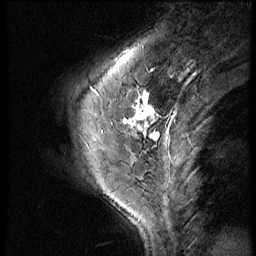
Breast MRI (dynamic contrast-enhanced), one sagittal slice; 3 images stored at this slice position (order not interpretable as contrast timing); 1.5 T; TE 4.2 ms, TR 9 ms; 2.5 mm slice thickness; 256 × 256 image matrix. Female patient, age 46 years. Case-level facts recorded for this patient, not image findings: setting: breast cancer imaged before/during neoadjuvant chemotherapy; receptor status: HER2-positive.
Annotated regions visible in this slice (semi-automatic segmentation, software-assisted and operator-edited):
- analysis volume of interest (the breast-tissue region the enhancement analysis was run in; not a lesion): bounding box [x1, y1, x2, y2] px = [73, 86, 164, 161]
- tumour enhancement mask (voxels above the 140 % enhancement threshold inside the analysis volume of interest): [124, 98, 158, 135]